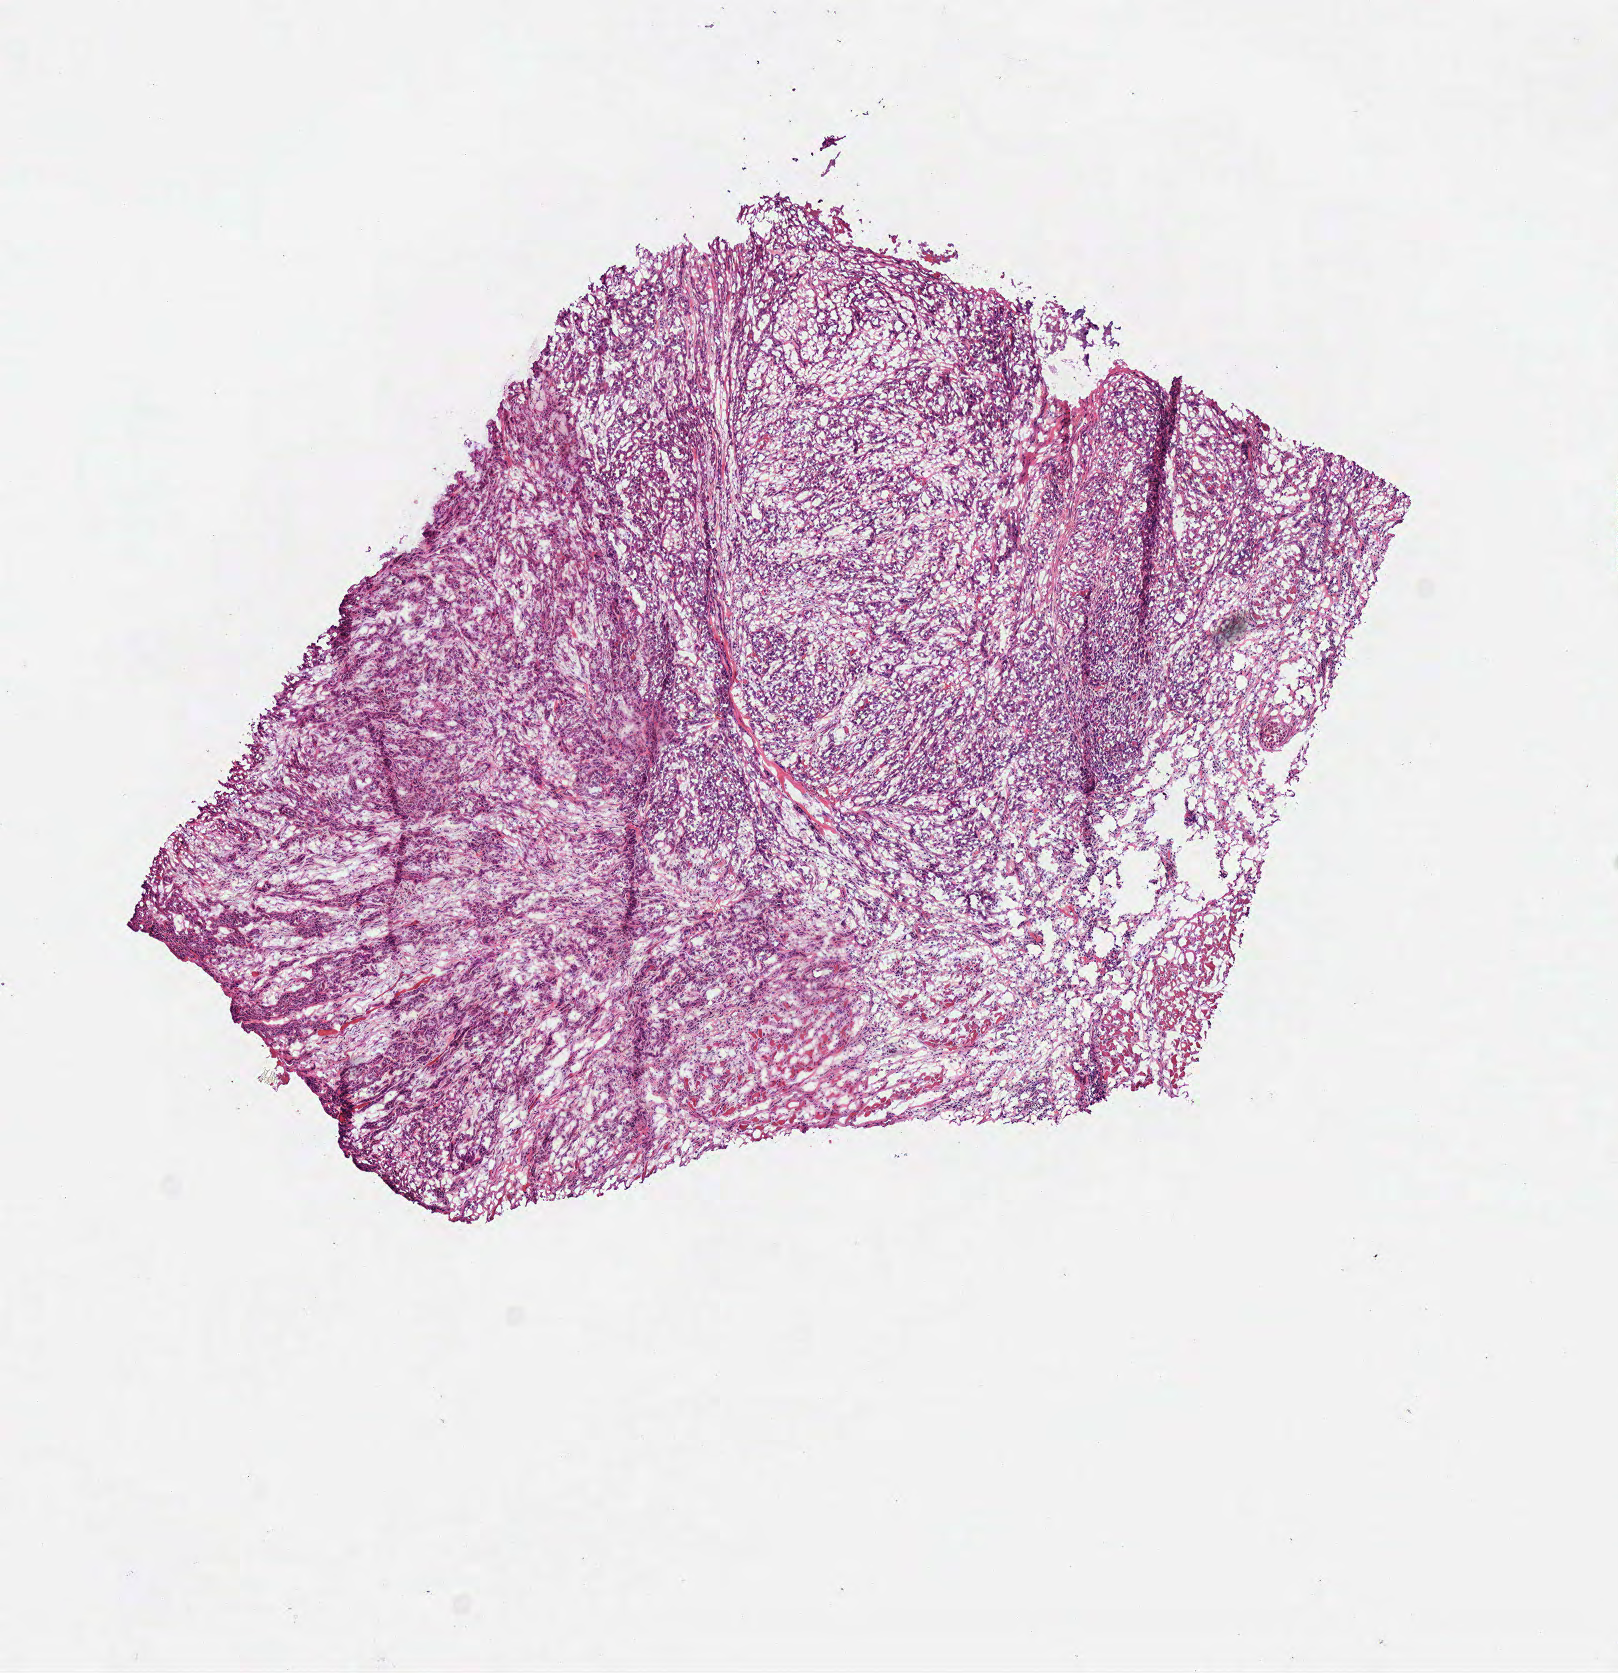
H&E whole-slide image — low-resolution overview of the scanned area, about 6.4 x 6.6 mm, frozen section from the top of the tissue portion, head and neck, primary tumour sample. Female, age 76 years at initial diagnosis.
Diagnosis: Squamous cell carcinoma, NOS (floor of mouth, NOS).